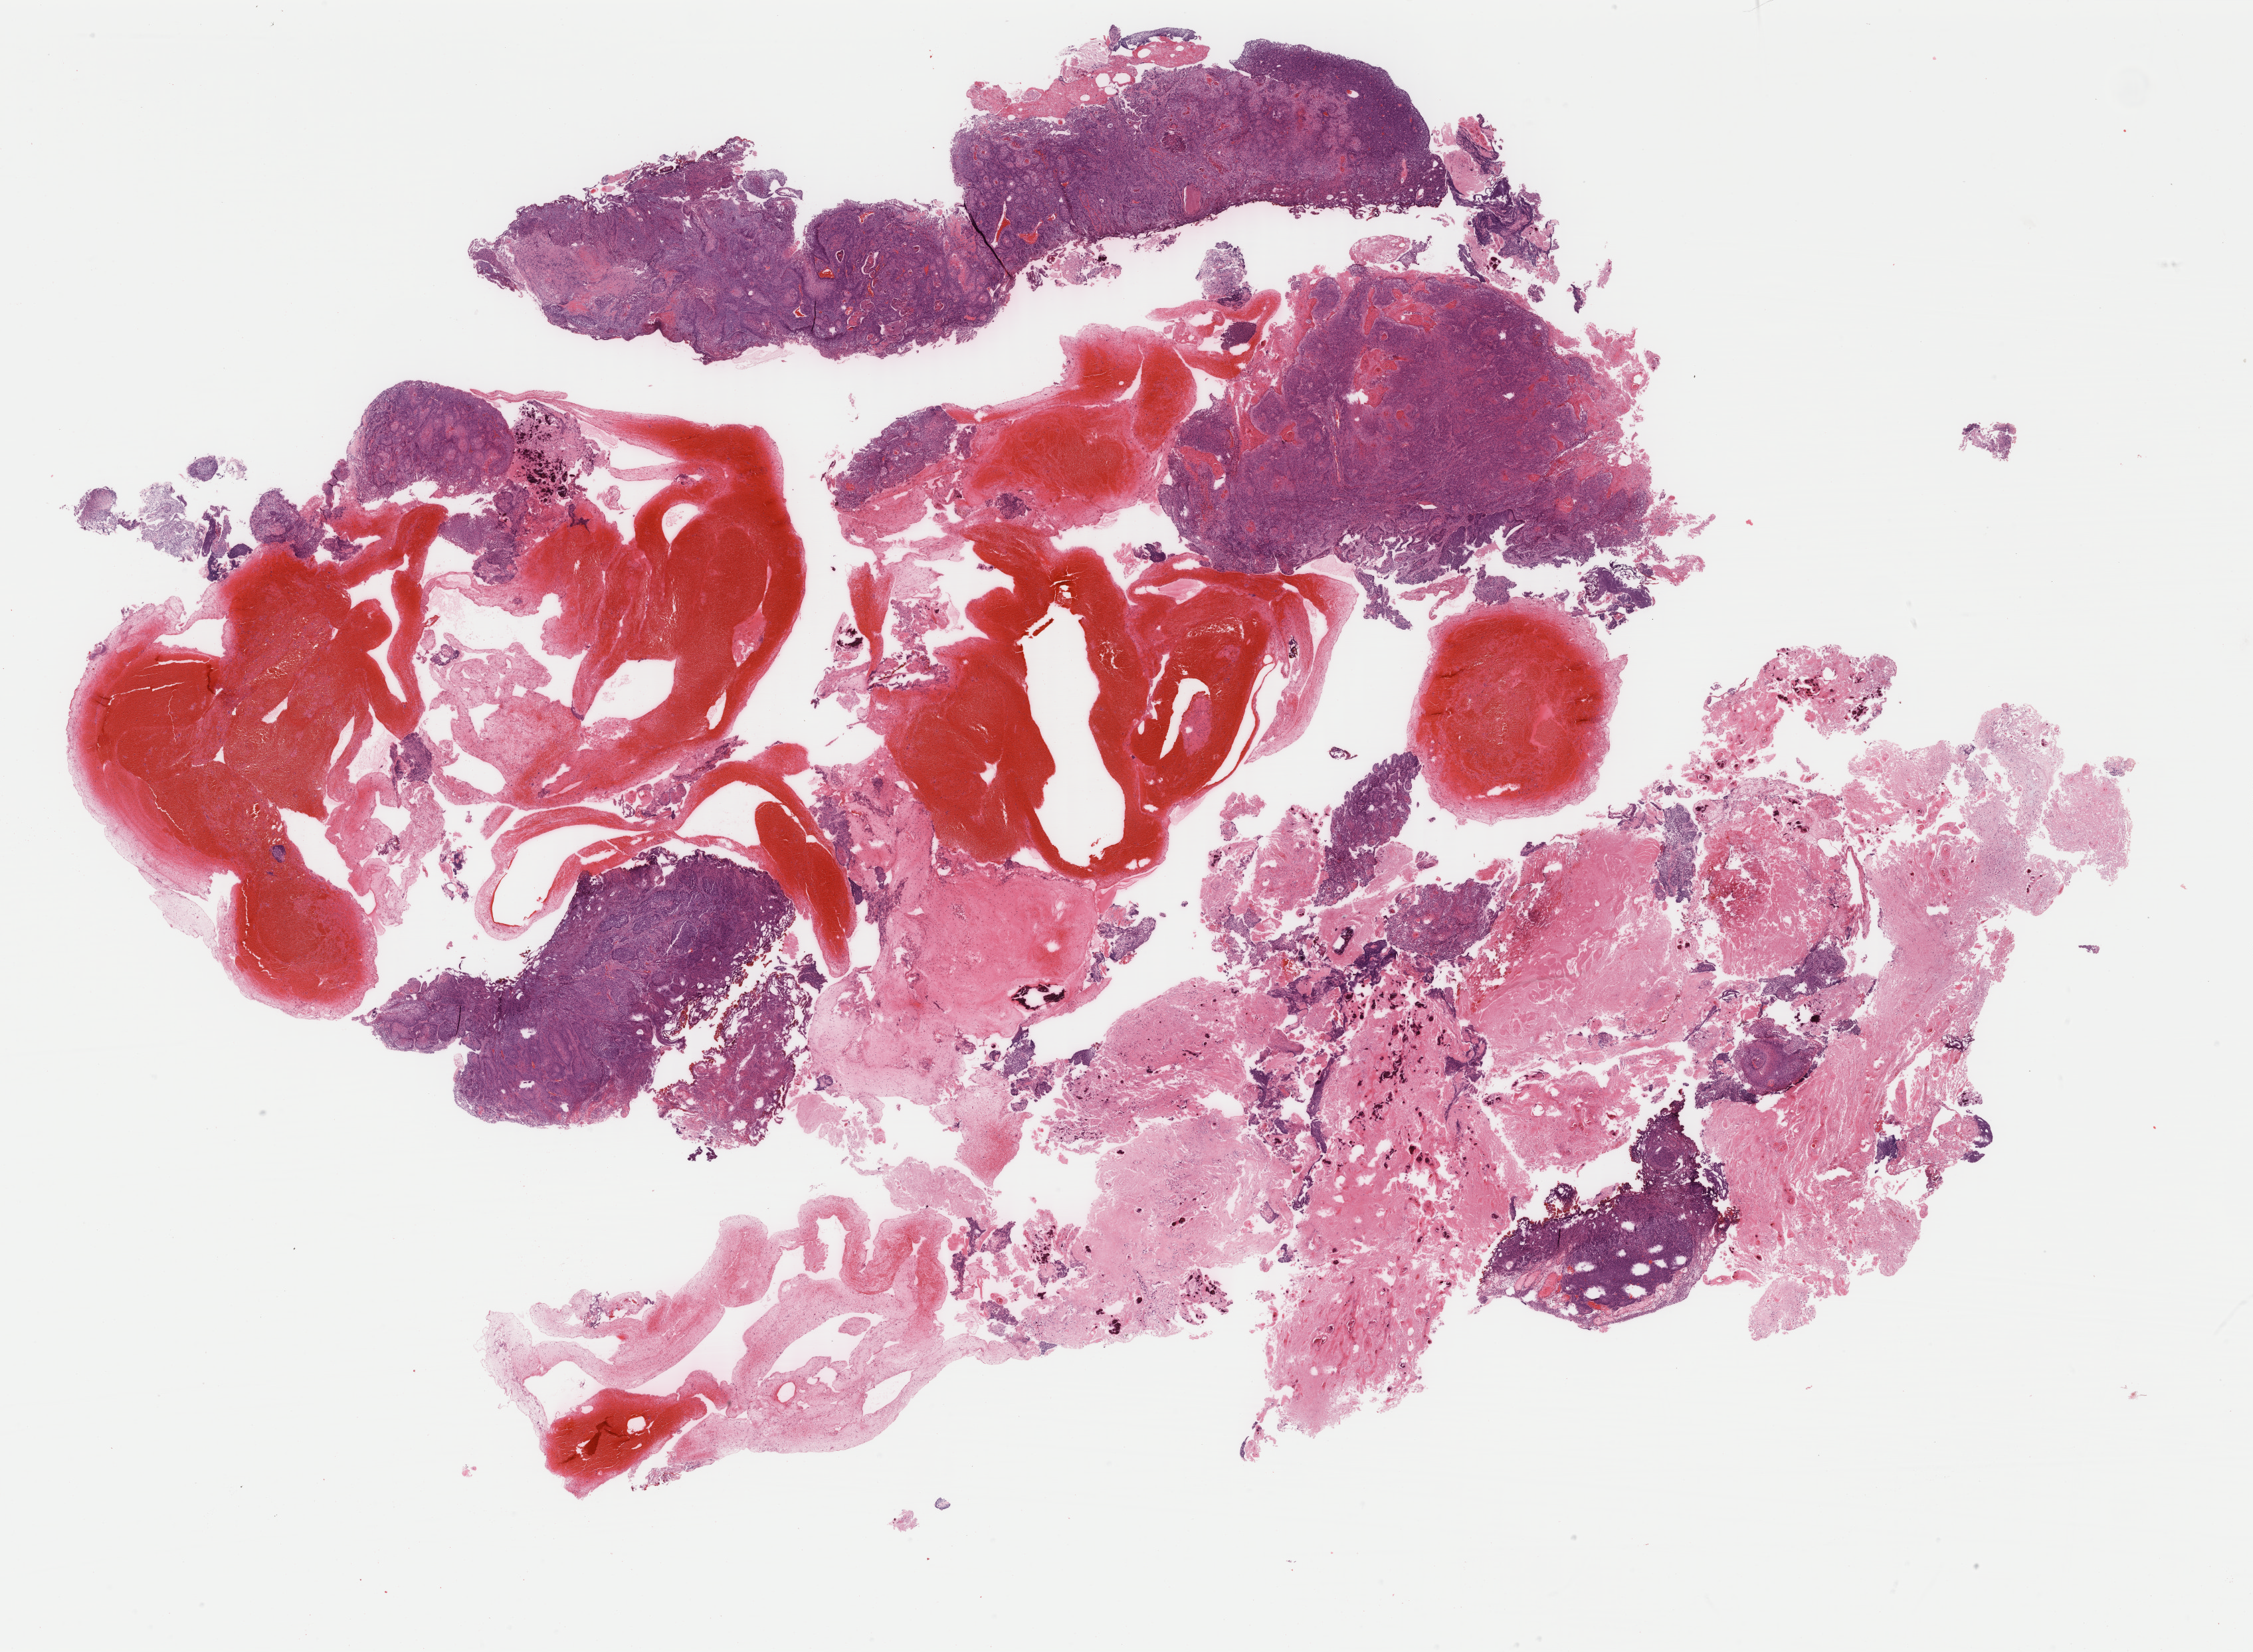
Digitized Hematoxylin and eosin (H&E) stained tissue section (whole slide) — a low-resolution overview of the entire scanned area, about 26.9 x 19.7 mm, FFPE section, primary tumour sample from the bladder. Male patient; age at initial diagnosis 66 years.
Histologic diagnosis: Transitional cell carcinoma.